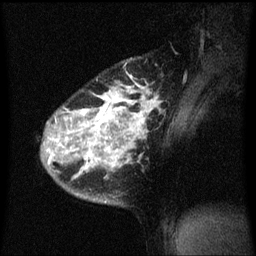
Breast MRI (dynamic contrast-enhanced), one sagittal slice. Slice 48 of 60 in the series (ordered by position). Dynamic contrast-enhanced series, image 2 of 3 at this slice position (ordered by acquisition). 1.5 T. TE 4.2 ms, TR 8.4 ms. 2 mm slice thickness. 256 × 256 image matrix, field of view 200 × 200 mm. Female patient, age 34 years. From the clinical record (not read from this slice): setting: breast cancer imaged before/during neoadjuvant chemotherapy; receptor status: HR-positive, HER2-negative.
Outlined on this slice (semi-automatically segmented with operator editing):
- analysis volume of interest (the breast-tissue region the enhancement analysis was run in; not a lesion): bounding box <38,56,163,205> (left, top, right, bottom; pixels)
- tumour enhancement mask (voxels above the 70 % enhancement threshold inside the analysis volume of interest): <48,76,157,177>